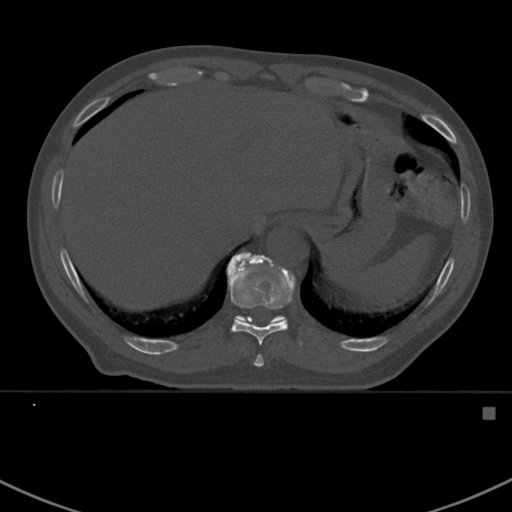
CT including the spine, one axial slice; reconstruction kernel Br40s; bone window (W 1800 / L 400 HU); 512 × 512 image matrix, field of view 358 × 358 mm. Patient: male, 59 years. From the clinical record (not read from this slice): primary cancer: prostate.
Outlined on this slice (semi-automatic segmentation, software-assisted and operator-edited):
- T10 vertebra: box from (x=227, y=256) to (x=301, y=367) px
- T11 vertebra: (x=227, y=253)–(x=296, y=322)
- T9 vertebra: (x=256, y=355)–(x=261, y=360)